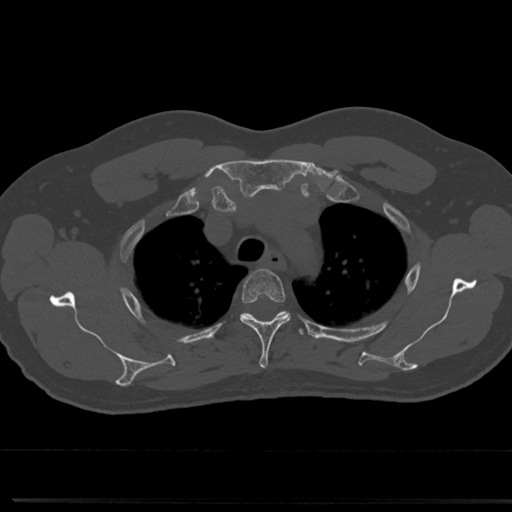
CT including the spine, one axial slice; position 582 of 817 along the scan axis; reconstruction kernel Br40s/3; 120 kVp; bone window (W 1800 / L 400 HU); 512 × 512 image matrix, field of view 355 × 355 mm. Male patient, age 61 years. From the clinical record (not read from this slice): primary cancer: prostate.
Structures marked on this image (semi-automatically segmented with operator editing):
- T3 vertebra: bounding box <239,270,290,369> (left, top, right, bottom; pixels)
- T4 vertebra: <222,310,308,342>